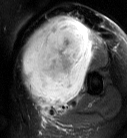
MRI of an extremity soft-tissue mass, one axial slice; position 46 of 87 along the scan axis; T2-weighted fat-saturated; MR volume resampled by the dataset authors to the PET/CT grid (not the native acquisition matrix); 3.27 mm slice thickness; 127 × 138 image matrix, field of view 124 × 135 mm. Female patient. Case-level facts recorded for this patient, not image findings: histological type: pleiomorphic leiomyosarcoma; grade: high; site of the primary tumour: left biceps.
Annotated regions visible in this slice (expert contour drawn on MRI and transferred to this co-registered scan by the dataset authors):
- gross tumour volume including surrounding oedema: box from (x=20, y=16) to (x=101, y=113) px
- gross tumour volume (mass): (x=22, y=16)–(x=94, y=106)